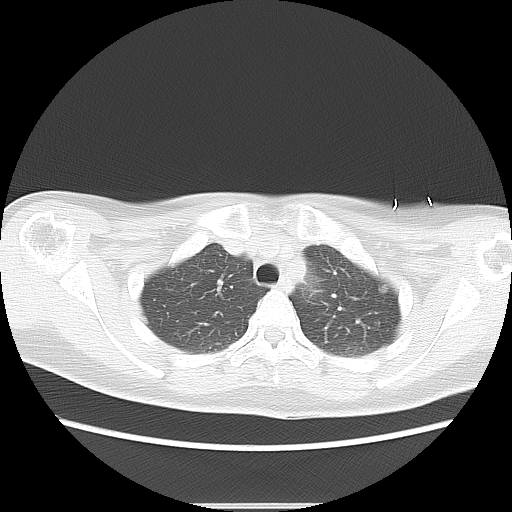
Chest CT, one axial slice. Slice 11 of 16 in the series (ordered by position). Reconstruction kernel LUNG. 120 kVp. Lung window (W 1500 / L -600 HU). 5 mm slice thickness. 512 × 512 image matrix. Female patient, age 42 years. Case-level facts recorded for this patient, not image findings: clinical TNM (as recorded): Tis N0 M0.
Structures marked on this image (bounding box drawn by a radiologist):
- lung tumour (recorded histology: adenocarcinoma): bounding box <371,278,390,298> (left, top, right, bottom; pixels)